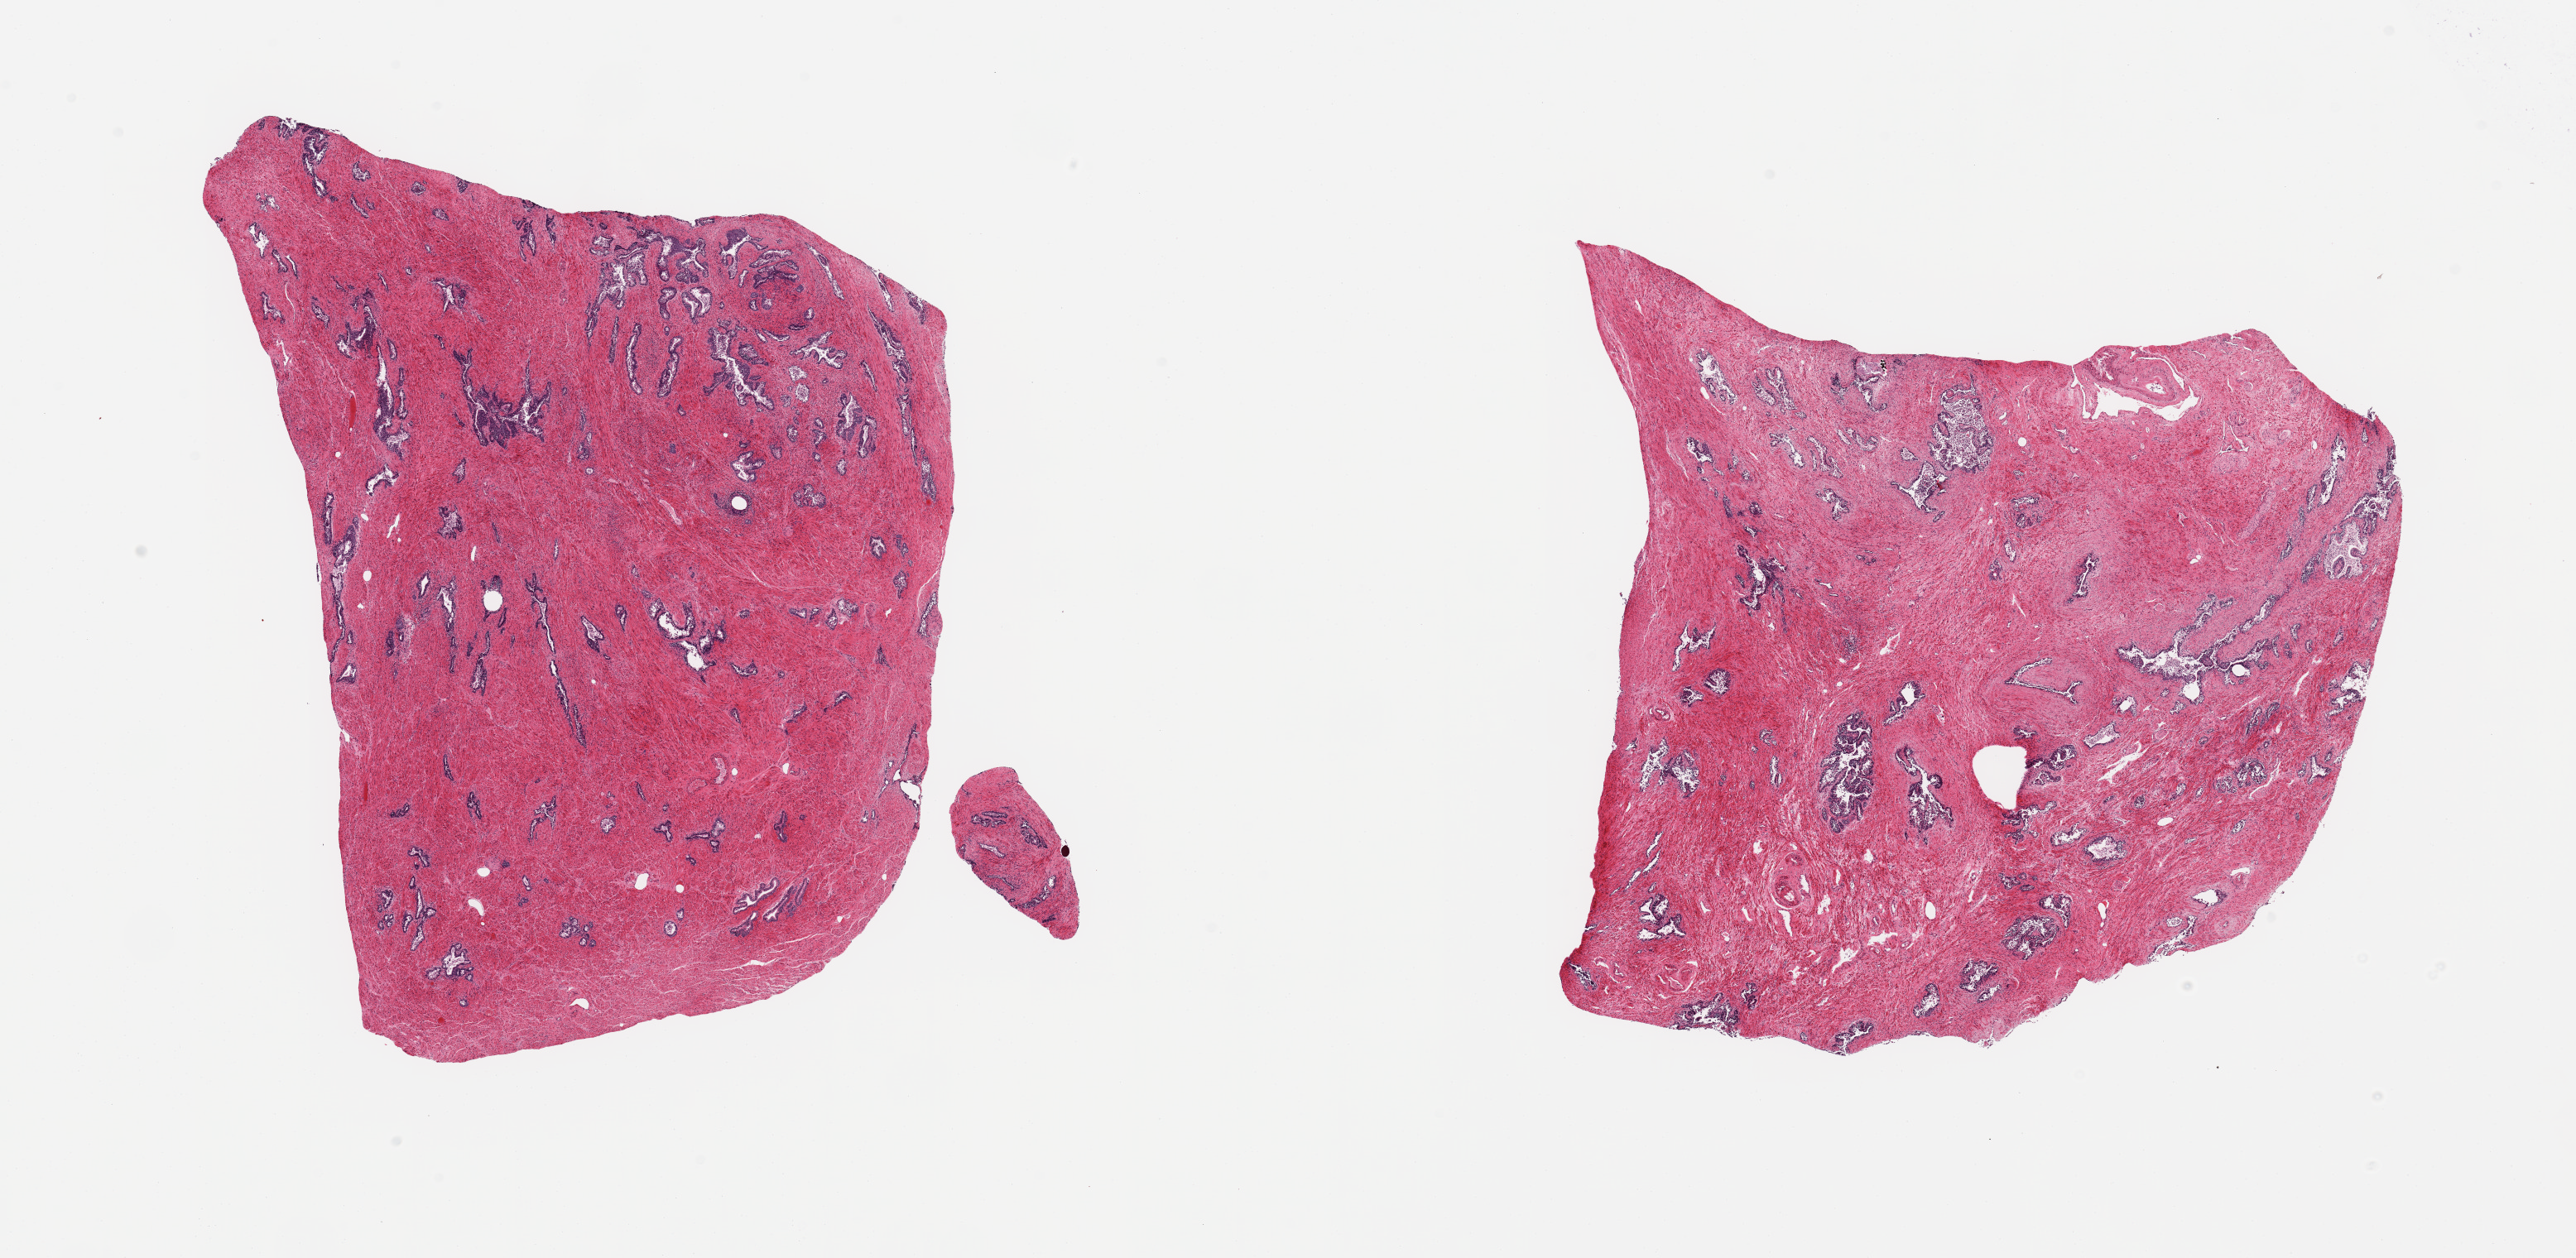
Whole-slide image, hematoxylin and eosin (H&E) stain — shown as a low-resolution overview of the whole scanned area (about 24.6 x 12.0 mm), PAXgene-fixed paraffin-embedded (PFPE) section, target tissue: prostate, tissue donor sample.
- reviewer comment on this tissue sample: 2 pieces; glands autolyzed, stroma intact